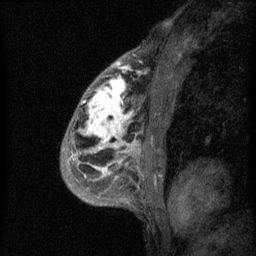
Breast MRI (dynamic contrast-enhanced), one sagittal slice. Position 38 of 60 along the scan axis. Dynamic contrast-enhanced series, image 2 of 3 at this slice position (ordered by acquisition). 1.5 T. TE 4.2 ms, TR 8 ms. 2 mm slice thickness. 256 × 256 image matrix, field of view 180 × 180 mm. Female patient, age 50 years.
Structures marked on this image (semi-automatically segmented with operator editing):
- analysis volume of interest (the breast-tissue region the enhancement analysis was run in; not a lesion): box from (x=66, y=64) to (x=141, y=187) px
- tumour enhancement mask (voxels above the 70 % enhancement threshold inside the analysis volume of interest): (x=81, y=64)–(x=141, y=177)